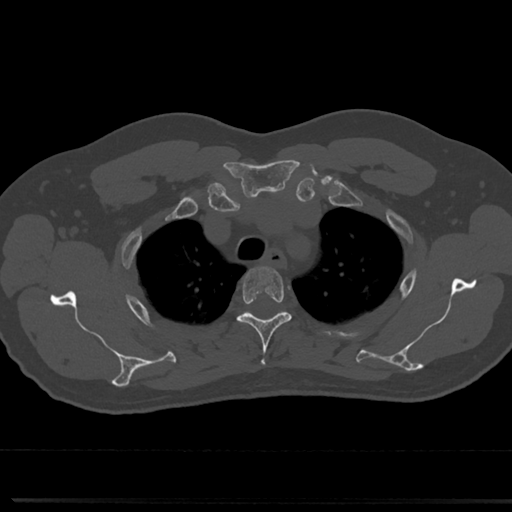
CT including the spine, one axial slice; position 588 of 817 along the scan axis; 120 kVp; bone window (W 1800 / L 400 HU); 512 × 512 image matrix, field of view 355 × 355 mm. Male patient, age 61 years. From the clinical record (not read from this slice): primary cancer: prostate.
Annotated regions visible in this slice (semi-automatically segmented with operator editing):
- T3 vertebra: box from (x=239, y=268) to (x=291, y=368) px
- T4 vertebra: (x=243, y=311)–(x=286, y=318)